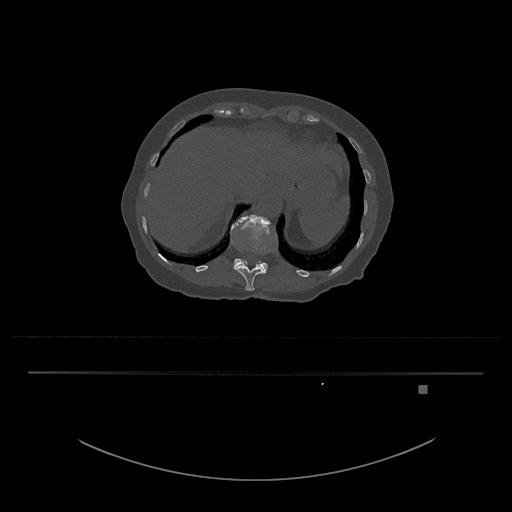
CT including the spine, one axial slice. Position 588 of 797 along the scan axis. Reconstruction kernel Br40s/3. 120 kVp. Bone window (W 1800 / L 400 HU). 0.5 mm slice thickness. 512 × 512 image matrix. Female patient, age 57 years. Case-level facts recorded for this patient, not image findings: primary cancer: cervical.
Structures marked on this image (semi-automatic segmentation, software-assisted and operator-edited):
- L1 vertebra: box from (x=230, y=214) to (x=278, y=272) px
- T12 vertebra: (x=235, y=261)–(x=266, y=291)